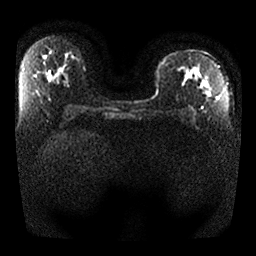
Breast MRI, one axial slice; position 14 of 25 along the scan axis; diffusion-weighted series; image 2 of 4 stored at this slice position (different b-values; order by instance number); 1.5 T; 4 mm slice thickness; 256 × 256 image matrix, field of view 330 × 330 mm. Female patient.
Outlined on this slice (manually delineated by an expert):
- tumour on diffusion-weighted imaging: bounding box (x1, y1, x2, y2) in pixels: (184, 66, 211, 97)